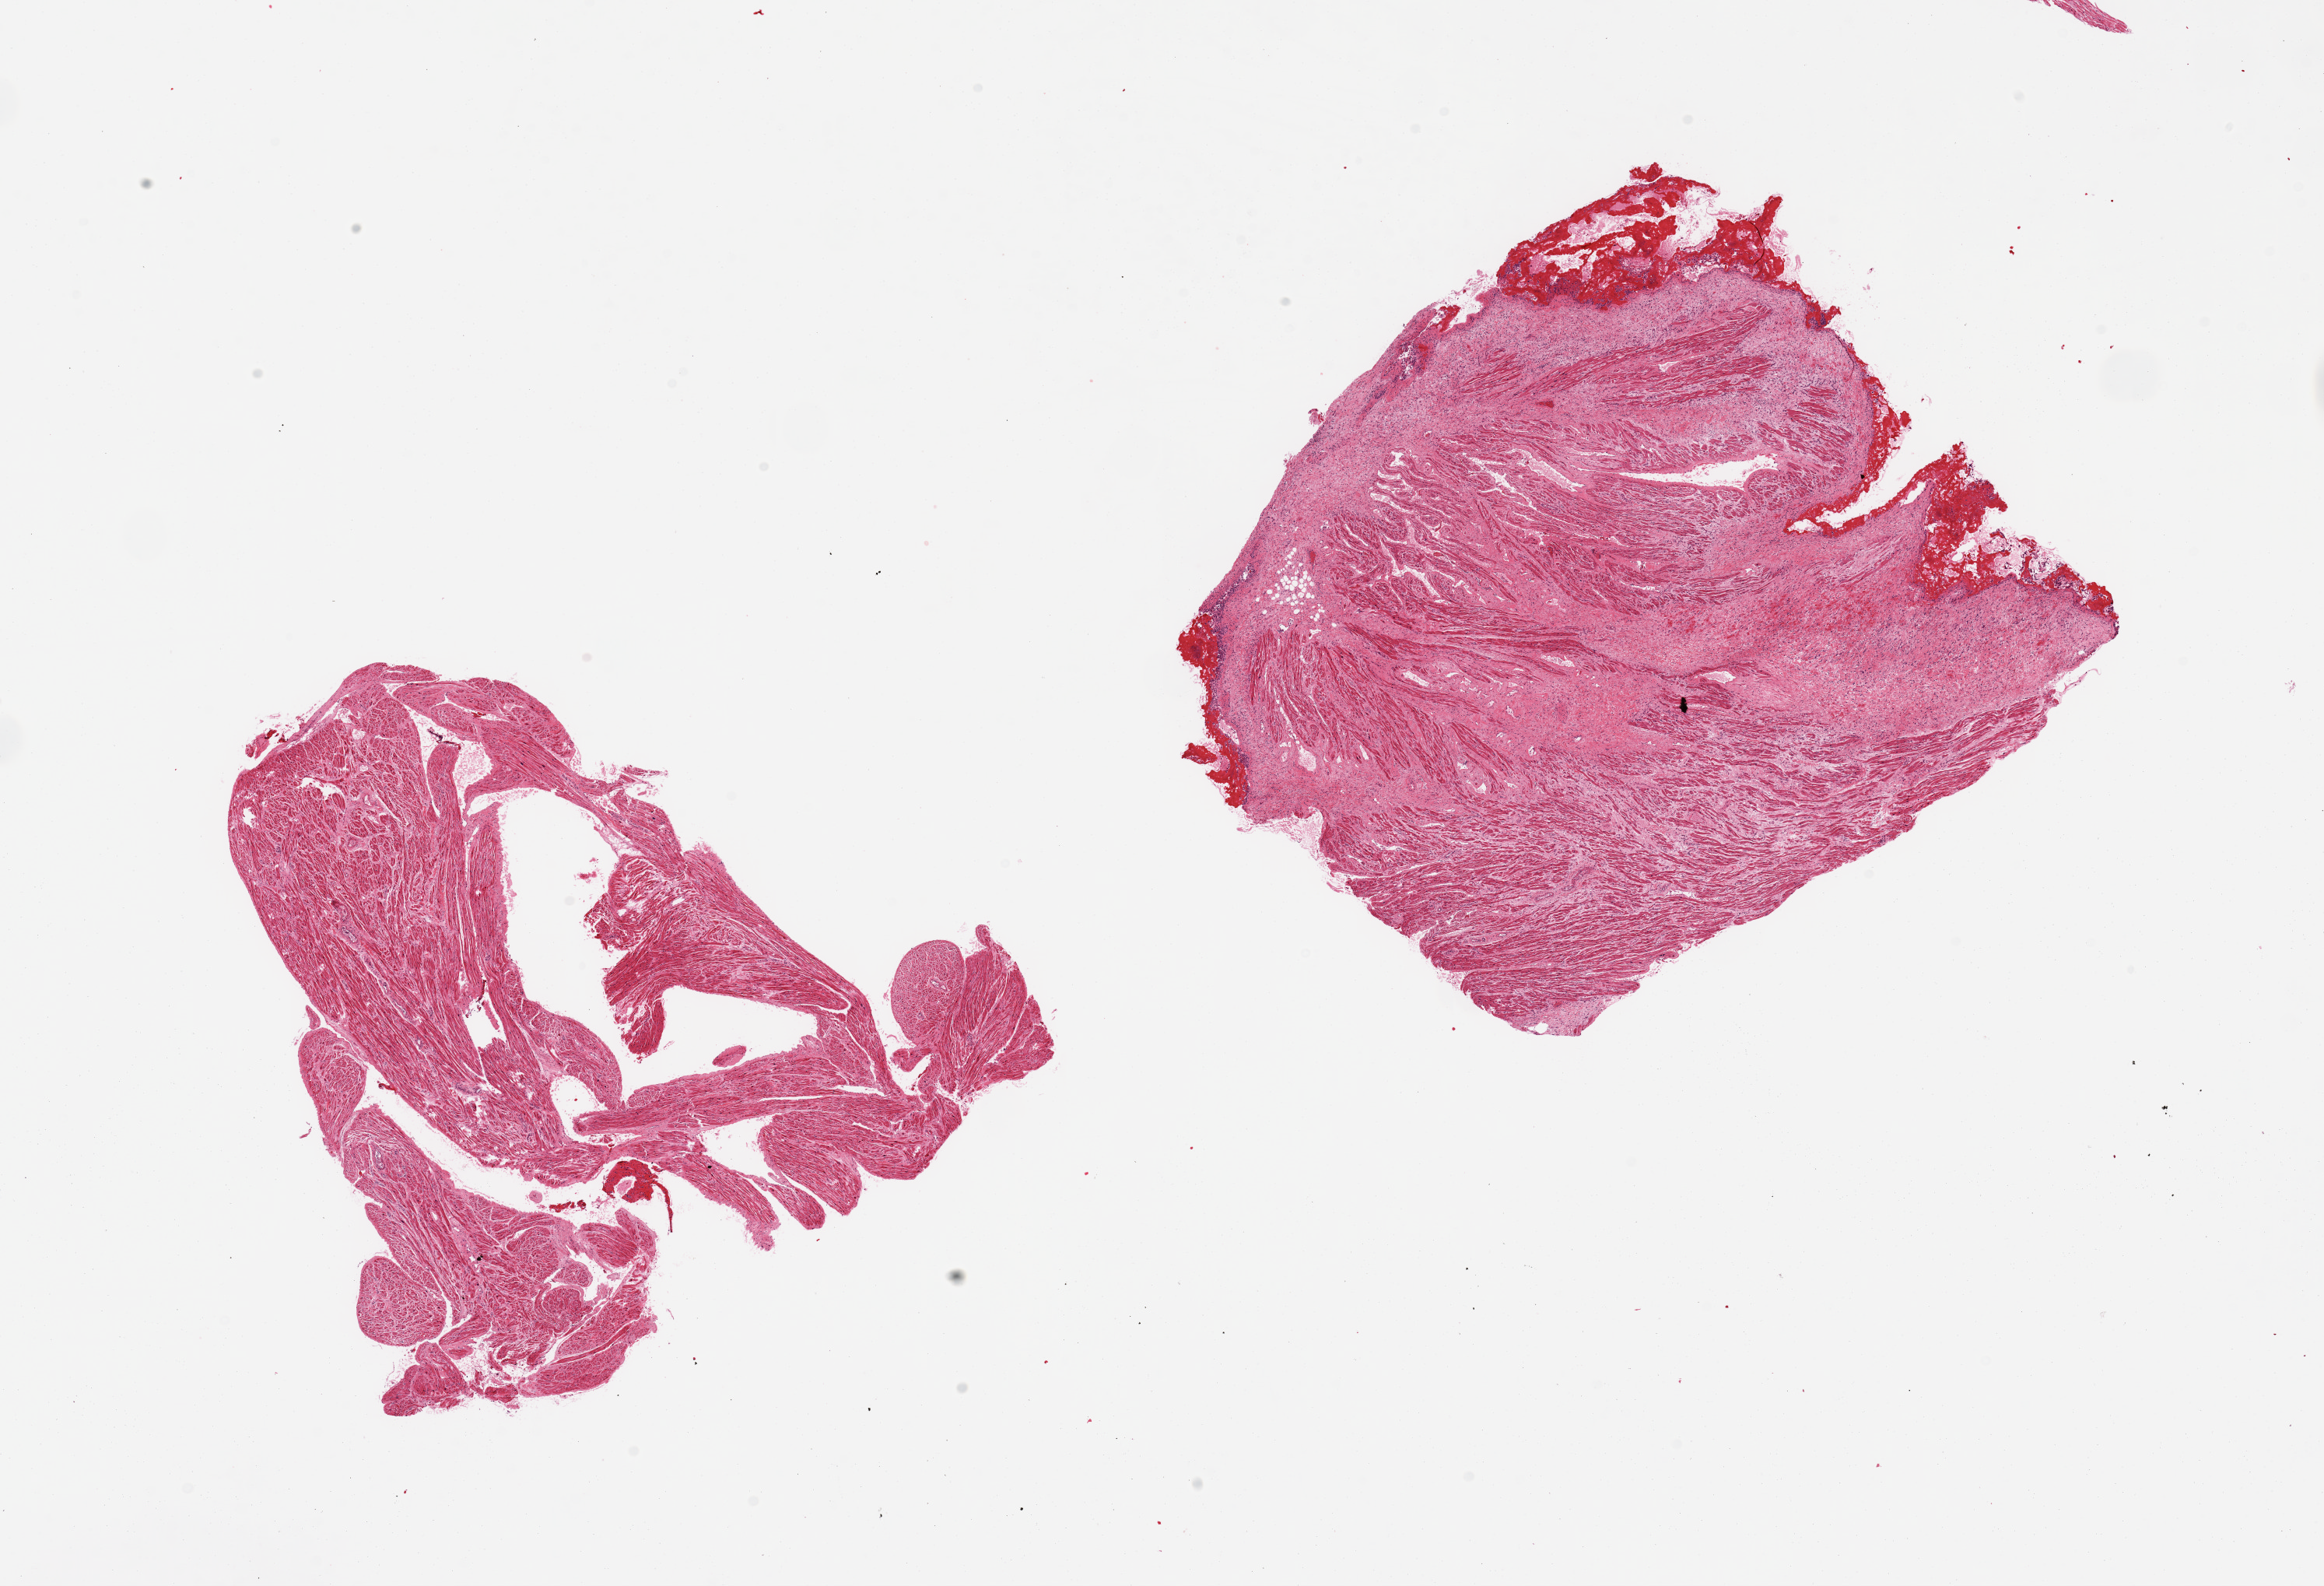
Whole-slide image, hematoxylin and eosin (H&E) stain — a low-resolution overview of the entire scanned area, about 23.6 x 16.1 mm; PAXgene-fixed paraffin-embedded (PFPE) section; sampled site (target tissue): auricular appendage; donor tissue sample. Donor sex: female.
Reviewer comment on this tissue sample: 2 pieces; fibromuscular tissue without extraneous fat.